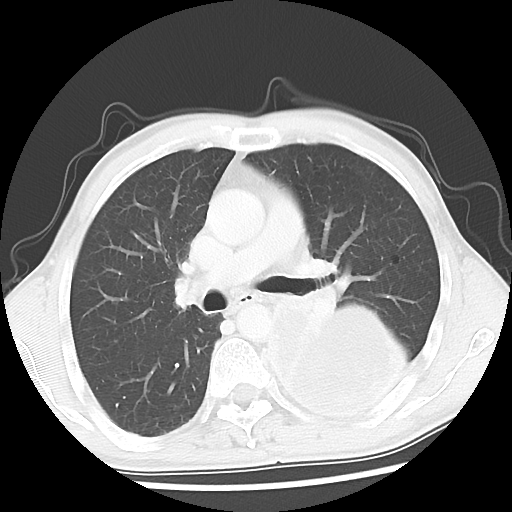
Chest CT, one axial slice. Slice 30 of 52 in the series (ordered by position). Reconstruction kernel LUNG. Lung window (W 1500 / L -600 HU). 5 mm slice thickness. 512 × 512 image matrix, field of view 318 × 318 mm. Male patient, age 60 years. From the clinical record (not read from this slice): clinical TNM (as recorded): T4 N0 M0.
Outlined on this slice (bounding box drawn by a radiologist):
- lung tumour (recorded histology: squamous cell carcinoma): bounding box (x1, y1, x2, y2) in pixels: (256, 298, 421, 422)